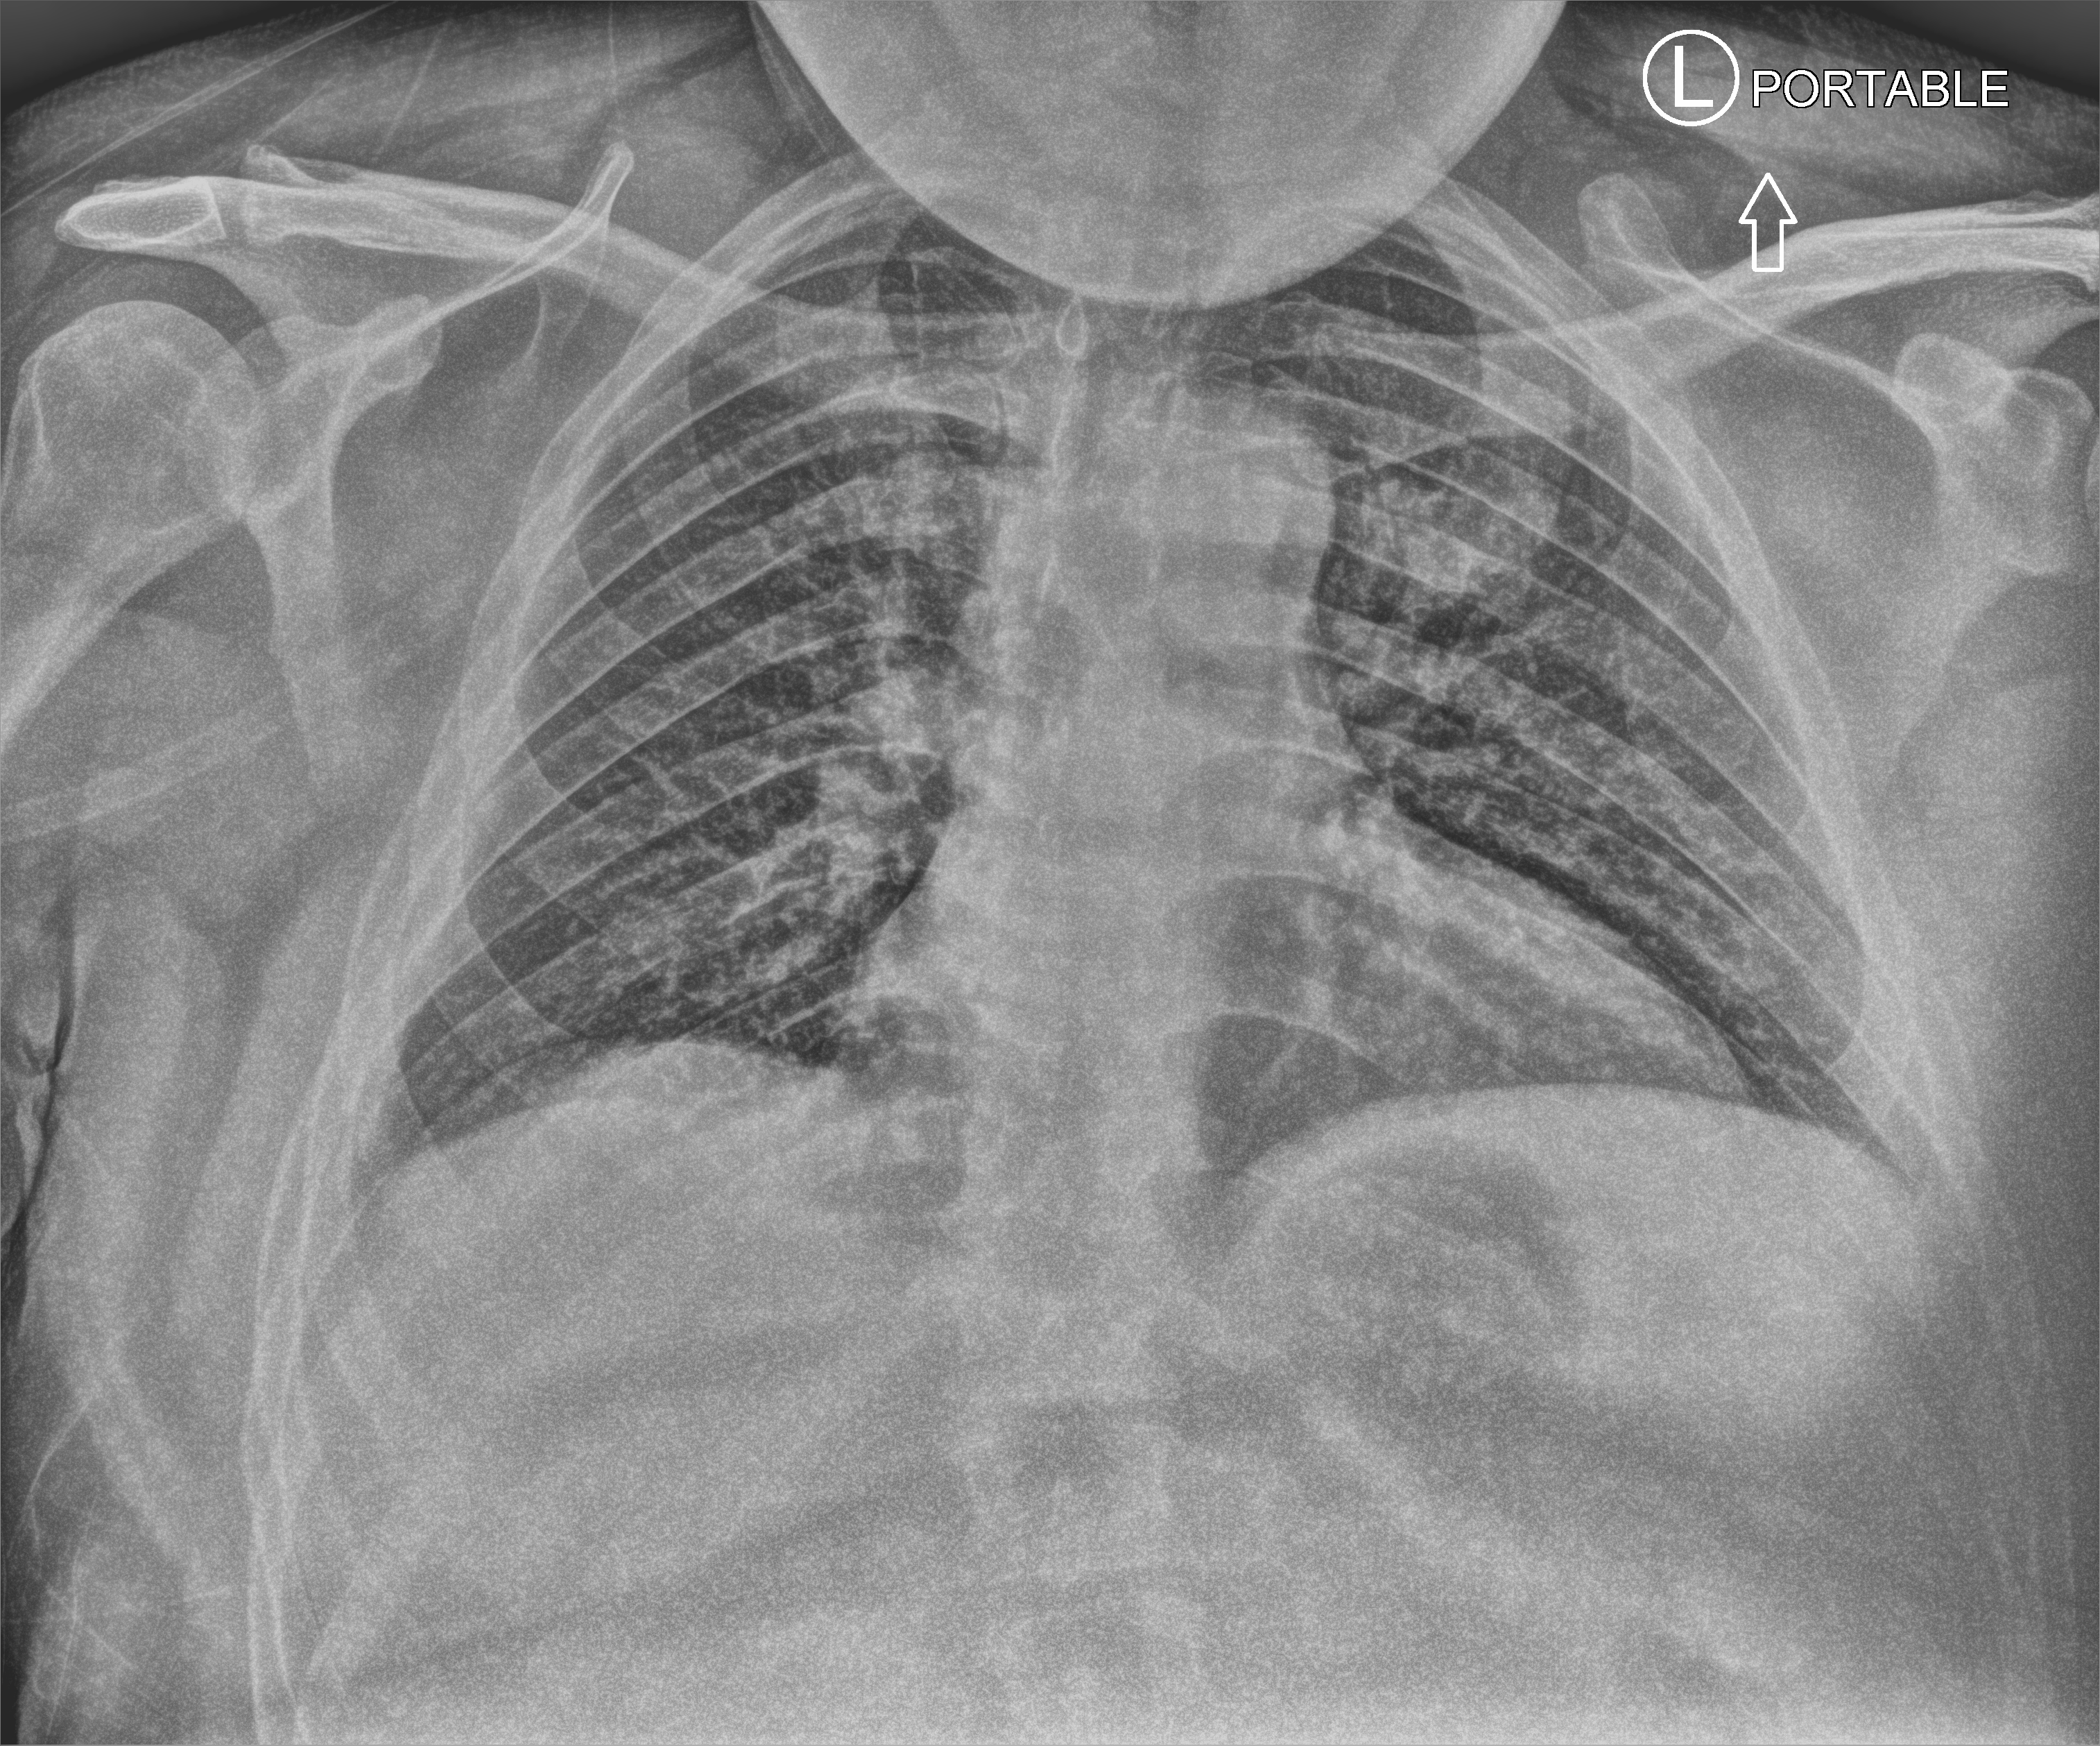
Chest X-ray (portable), anteroposterior (AP) projection. Patient hospitalised with COVID-19; male, aged 18–59 years.
Hospital-stay facts (about this admission, not read from this image; timing relative to this image not recorded):
- mechanically ventilated during this hospital stay: no